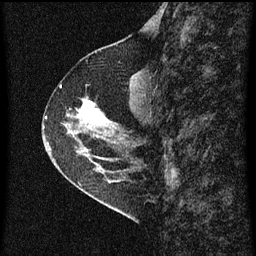
Breast MRI (dynamic contrast-enhanced), one sagittal slice; dynamic contrast-enhanced series, image 2 of 3 at this slice position (ordered by acquisition); 1.5 T; TE 4.2 ms, TR 8 ms; 2 mm slice thickness; 256 × 256 image matrix, field of view 180 × 180 mm. Female patient, age 56 years.
Annotated regions visible in this slice (semi-automatically segmented with operator editing):
- analysis volume of interest (the breast-tissue region the enhancement analysis was run in; not a lesion): bounding box (x1, y1, x2, y2) in pixels: (49, 96, 110, 159)
- tumour enhancement mask (voxels above the 70 % enhancement threshold inside the analysis volume of interest): (78, 100, 103, 123)